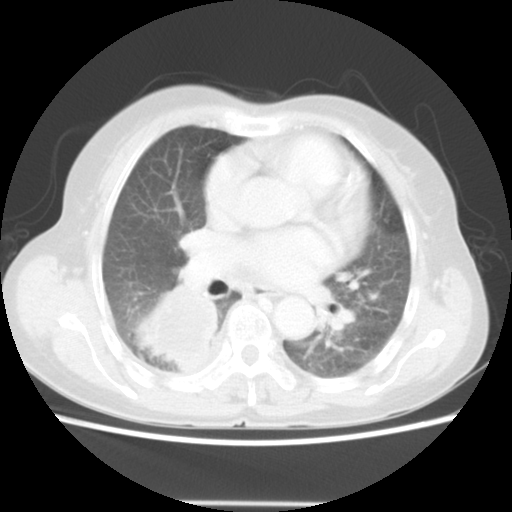
Chest CT, one axial slice; slice 27 of 52 in the series (ordered by position); 140 kVp; lung window (W 1500 / L -600 HU); 5 mm slice thickness; 512 × 512 image matrix, field of view 337 × 337 mm. Female patient, age 67 years. Case-level facts recorded for this patient, not image findings: clinical TNM (as recorded): T3 N1 M1.
Structures marked on this image (bounding box drawn by a radiologist):
- lung tumour (recorded histology: adenocarcinoma): bounding box <134,281,220,373> (left, top, right, bottom; pixels)